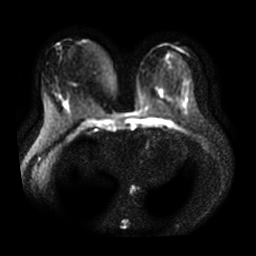
Breast MRI, one axial slice. Slice 18 of 35 in the series (ordered by position). Diffusion-weighted series; image 2 of 4 stored at this slice position (different b-values; order by instance number). 3 T. 256 × 256 image matrix. Female patient.
Structures marked on this image (expert manual segmentation):
- tumour on diffusion-weighted imaging: bounding box <64,102,68,108> (left, top, right, bottom; pixels)